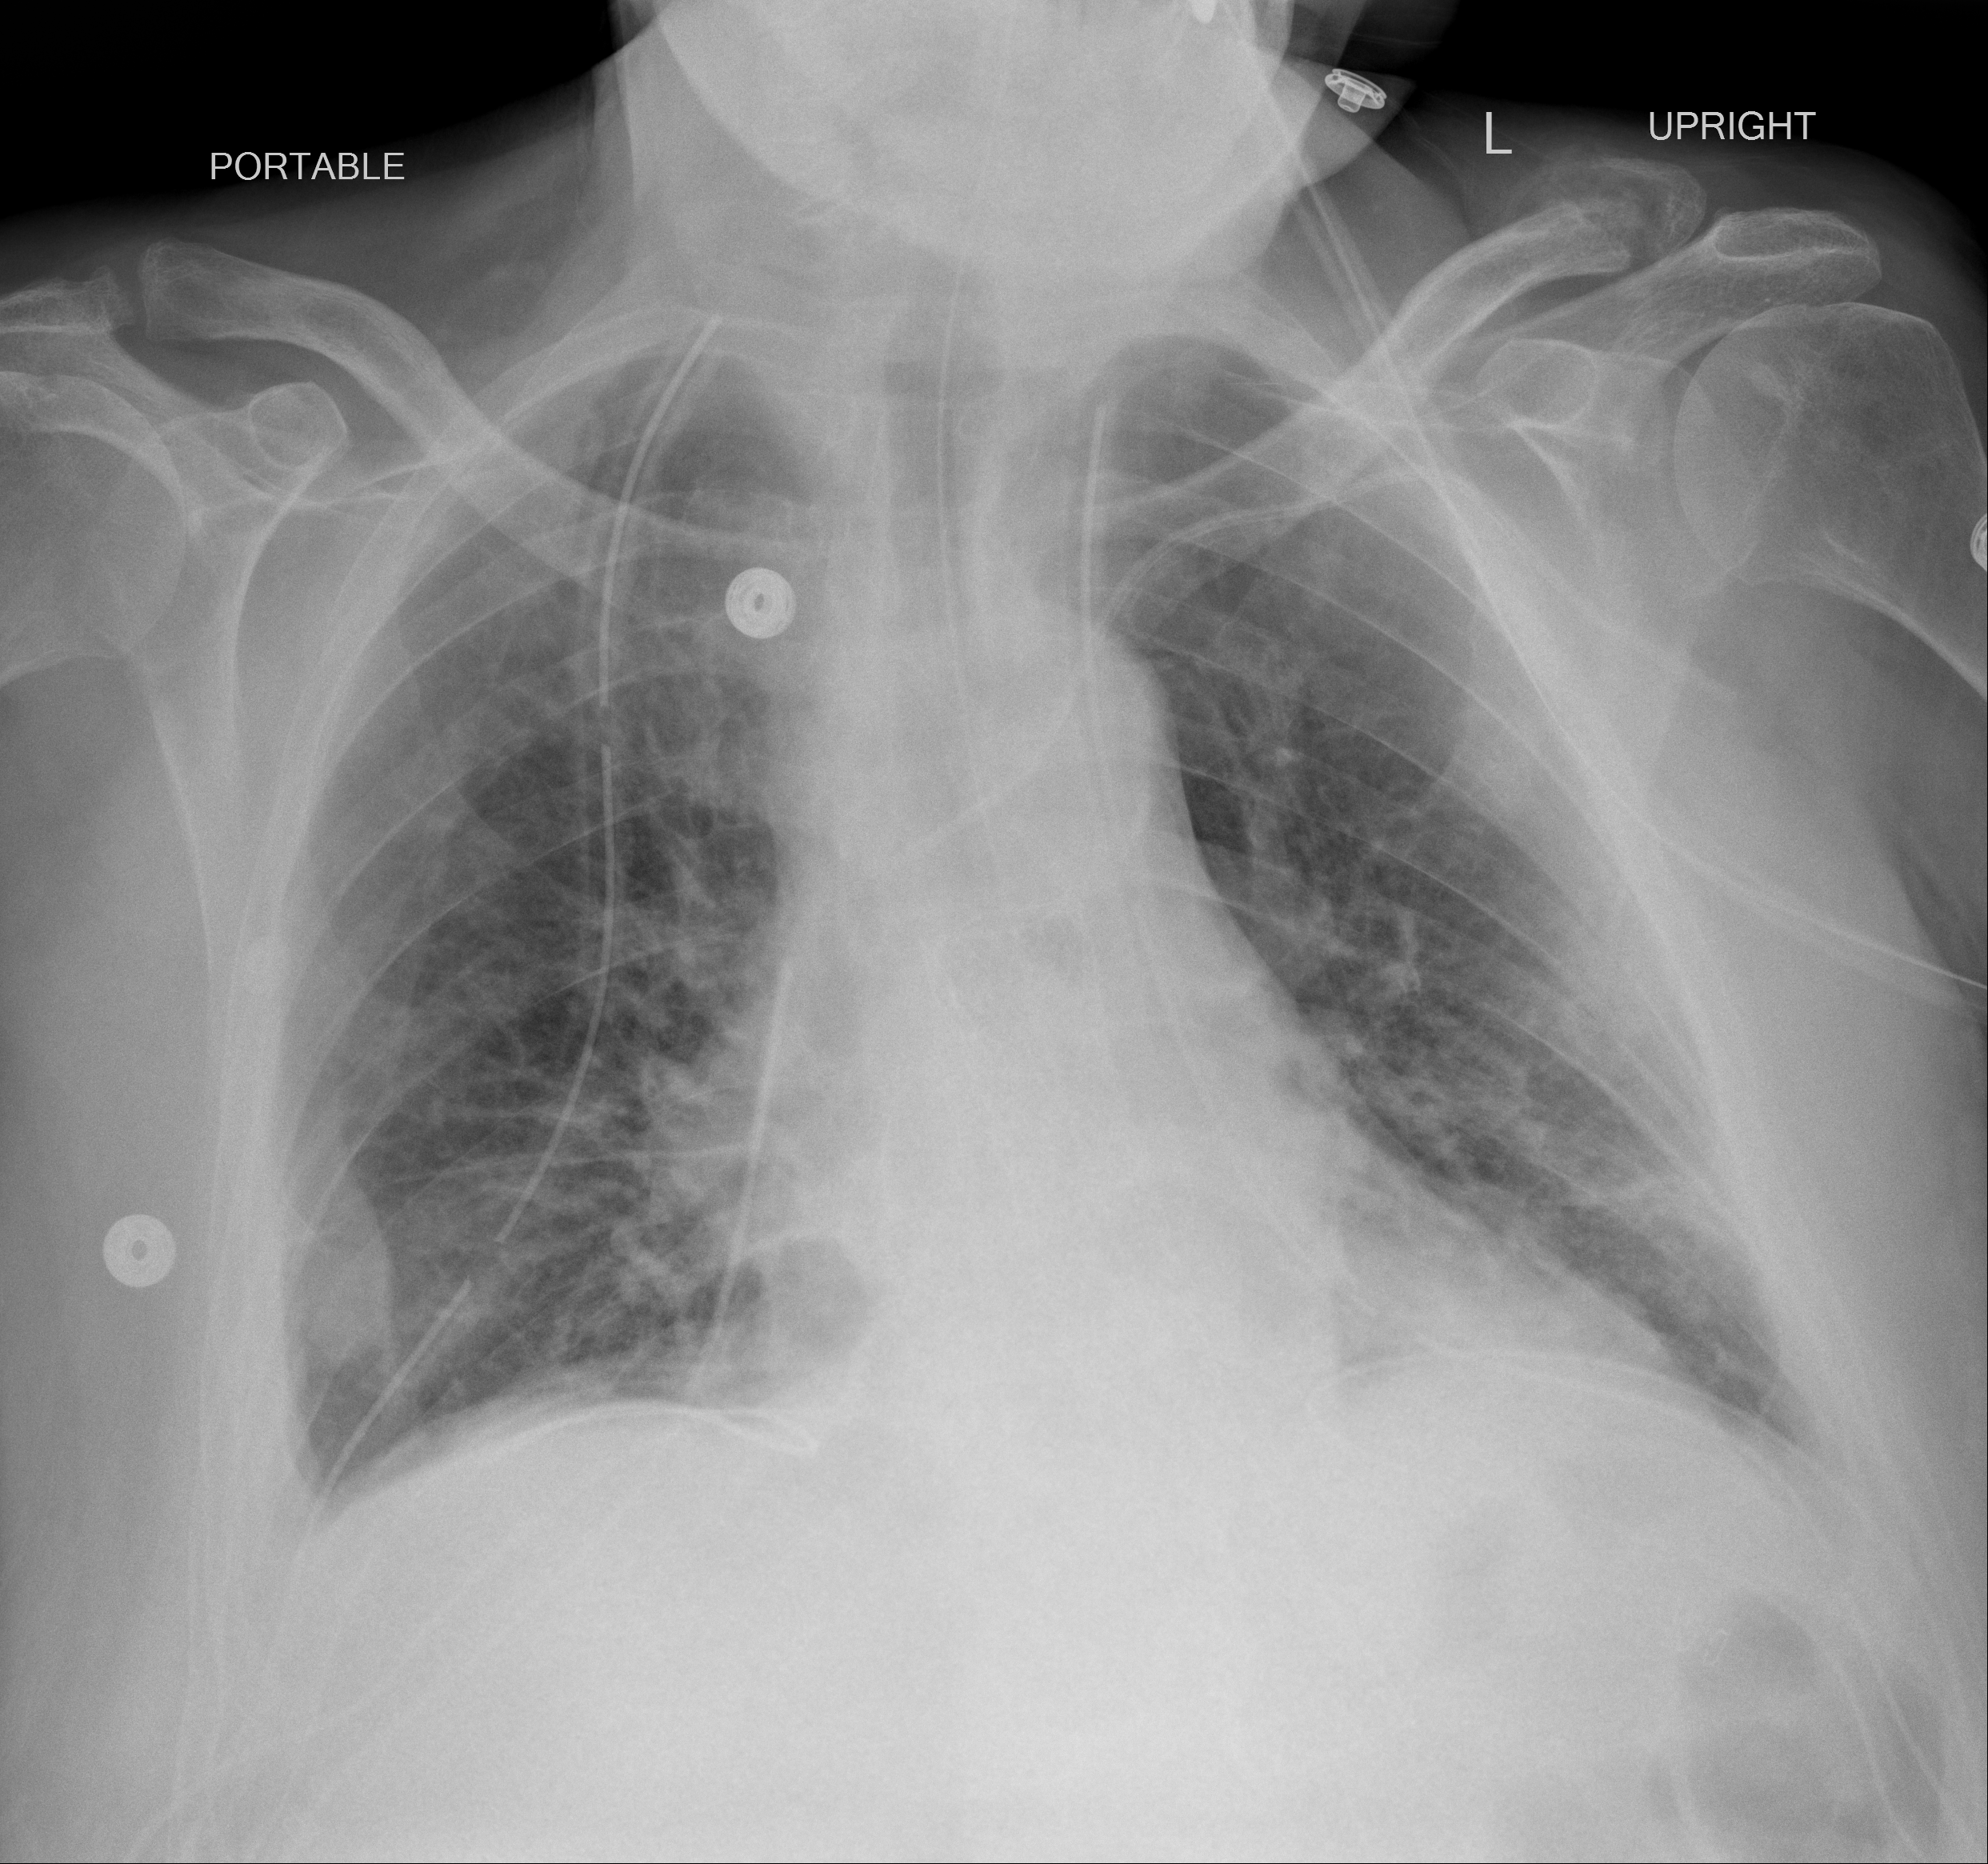
Chest X-ray (portable), AP projection. Male patient, age 64 years; COVID-19 (test-positive).
Radiologist's key findings for this exam: Linear opacities are seen within the bilateral lung bases with a small right-sided pleural effusion.